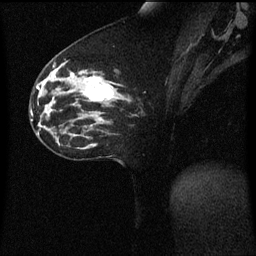
Breast MRI (dynamic contrast-enhanced), one sagittal slice; slice 30 of 60 in the series (ordered by position); dynamic contrast-enhanced series, image 2 of 3 at this slice position (ordered by acquisition); 1.5 T; TE 4.2 ms, TR 8.4 ms; 256 × 256 image matrix, field of view 200 × 200 mm. Female patient, age 33 years. Case-level facts recorded for this patient, not image findings: setting: breast cancer imaged before/during neoadjuvant chemotherapy; receptor status: triple-negative.
Outlined on this slice (semi-automatic segmentation, software-assisted and operator-edited):
- analysis volume of interest (the breast-tissue region the enhancement analysis was run in; not a lesion): bounding box [x1, y1, x2, y2] px = [76, 70, 123, 113]
- tumour enhancement mask (voxels above the 70 % enhancement threshold inside the analysis volume of interest): [82, 76, 113, 101]